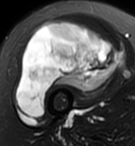
MRI of an extremity soft-tissue mass, one axial slice; T2-weighted fat-saturated; MR volume resampled by the dataset authors to the PET/CT grid (not the native acquisition matrix); 3.27 mm slice thickness; 135 × 146 image matrix, field of view 132 × 143 mm. Female patient. From the clinical record (not read from this slice): histological type: pleiomorphic undifferentiated sarcoma; grade: high; site of the primary tumour: right quadricep.
Structures marked on this image (expert contour drawn on MRI and transferred to this co-registered scan by the dataset authors):
- gross tumour volume including surrounding oedema: bounding box <16,20,120,119> (left, top, right, bottom; pixels)
- gross tumour volume (mass): <16,20,120,119>